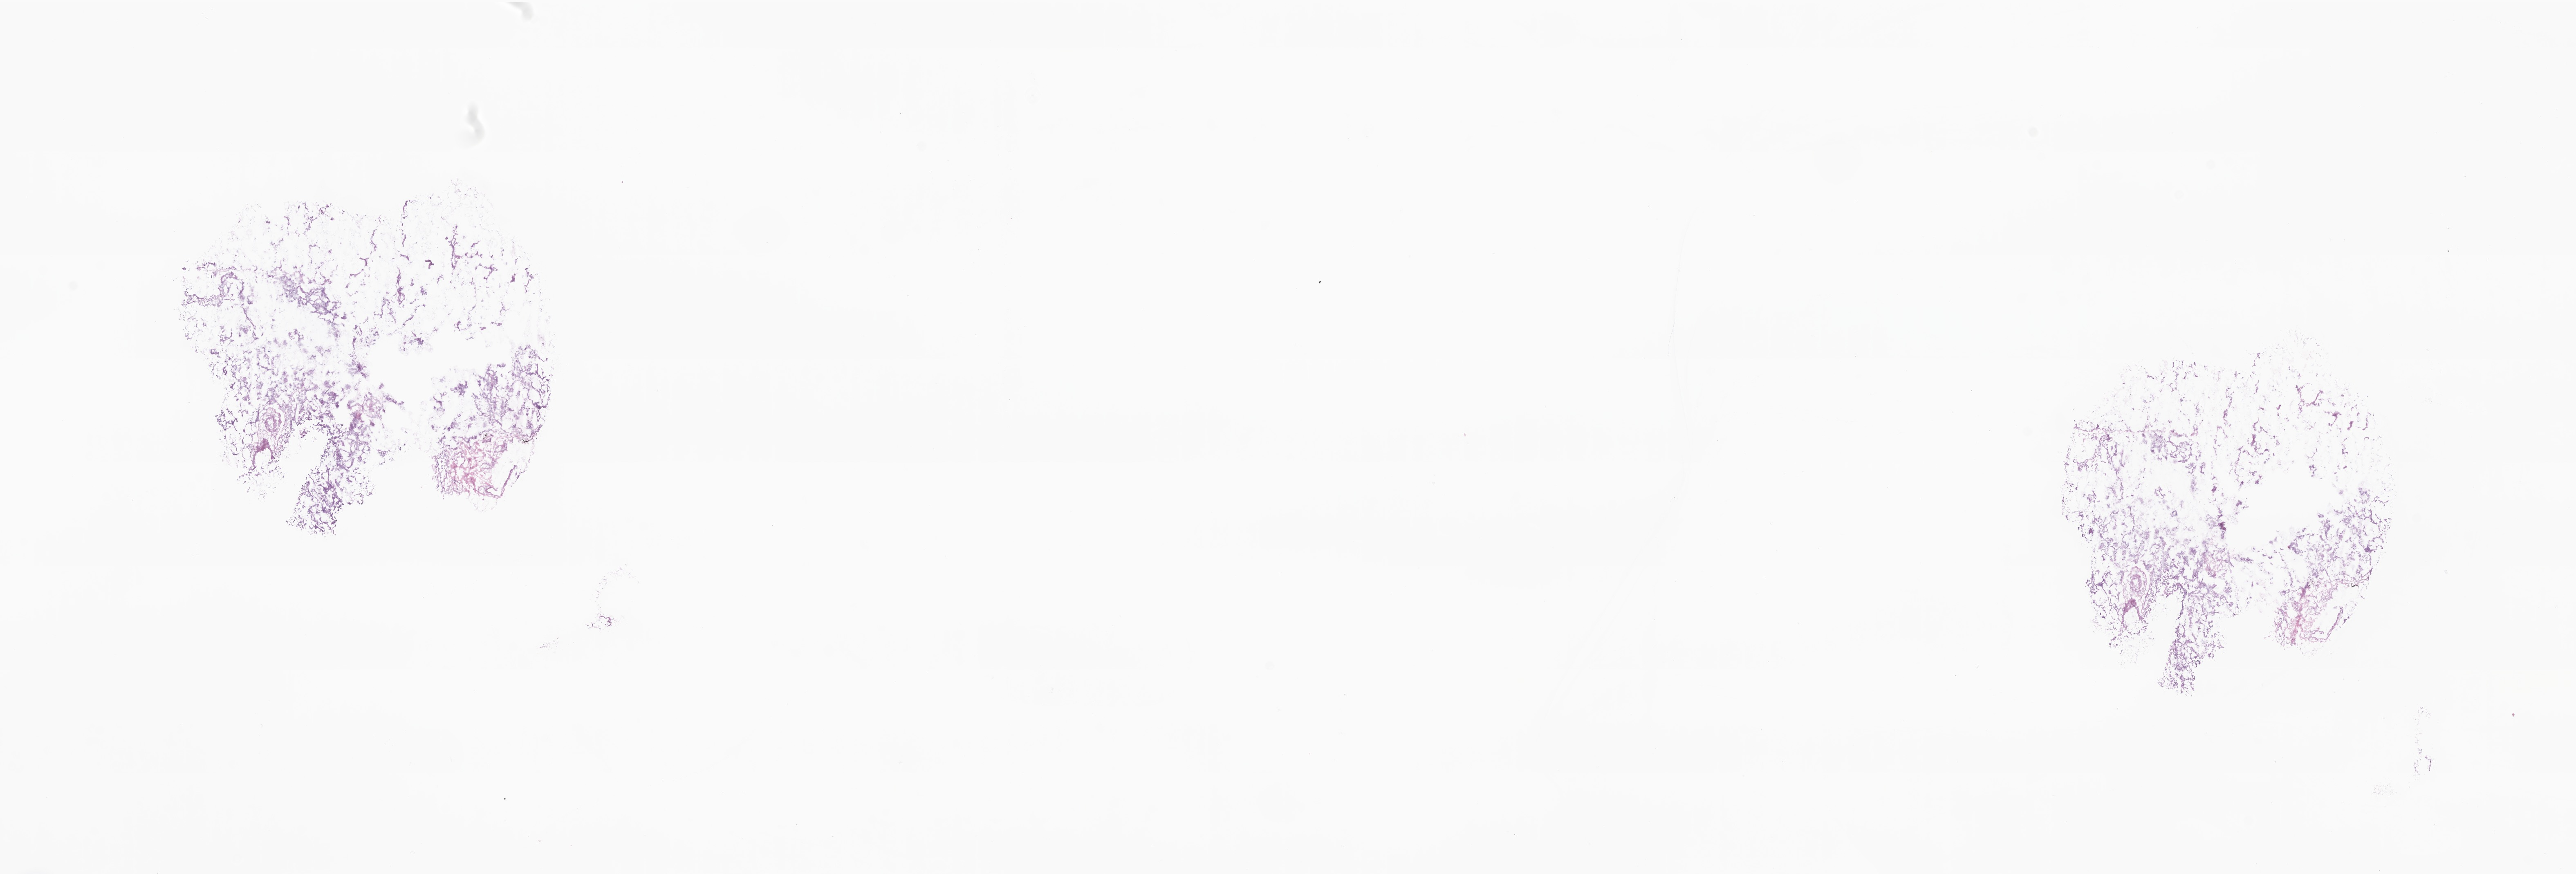
Digitized H&E-stained section — low-resolution overview of the scanned area, about 26.6 x 9.0 mm, cryosection, primary tumor, site: middle lobe of right lung. Male patient; age at initial diagnosis 76 years. Pathologist review of this section (percent, as recorded): tumor cells 15%, tumor nuclei 26%, stromal cells 30%, necrosis 30%, normal cells 25%. Inflammatory infiltration, as recorded: lymphocyte infiltration 0%, monocyte infiltration 0%, neutrophil infiltration 0%.
- section: bottom of the tissue portion
- diagnosis: Minimally invasive adenocarcinoma, mucinous